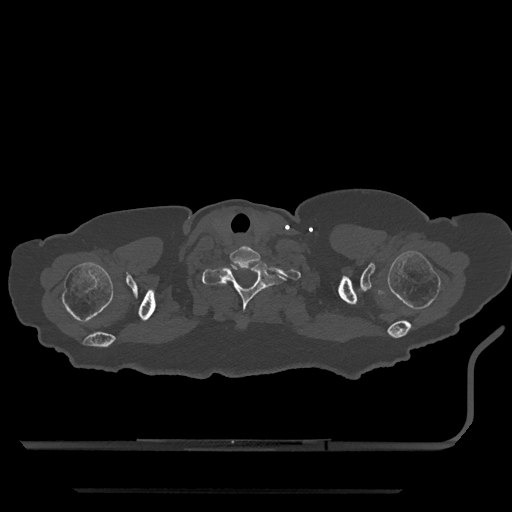
CT including the spine, one axial slice. Slice 717 of 797 in the series (ordered by position). 120 kVp. Bone window (W 1800 / L 400 HU). 0.5 mm slice thickness. 512 × 512 image matrix, field of view 440 × 440 mm. Female patient, age 51 years. Case-level facts recorded for this patient, not image findings: primary cancer: neuro.
Structures marked on this image (semi-automatic segmentation, software-assisted and operator-edited):
- T1 vertebra: bounding box [x1, y1, x2, y2] px = [202, 262, 286, 312]